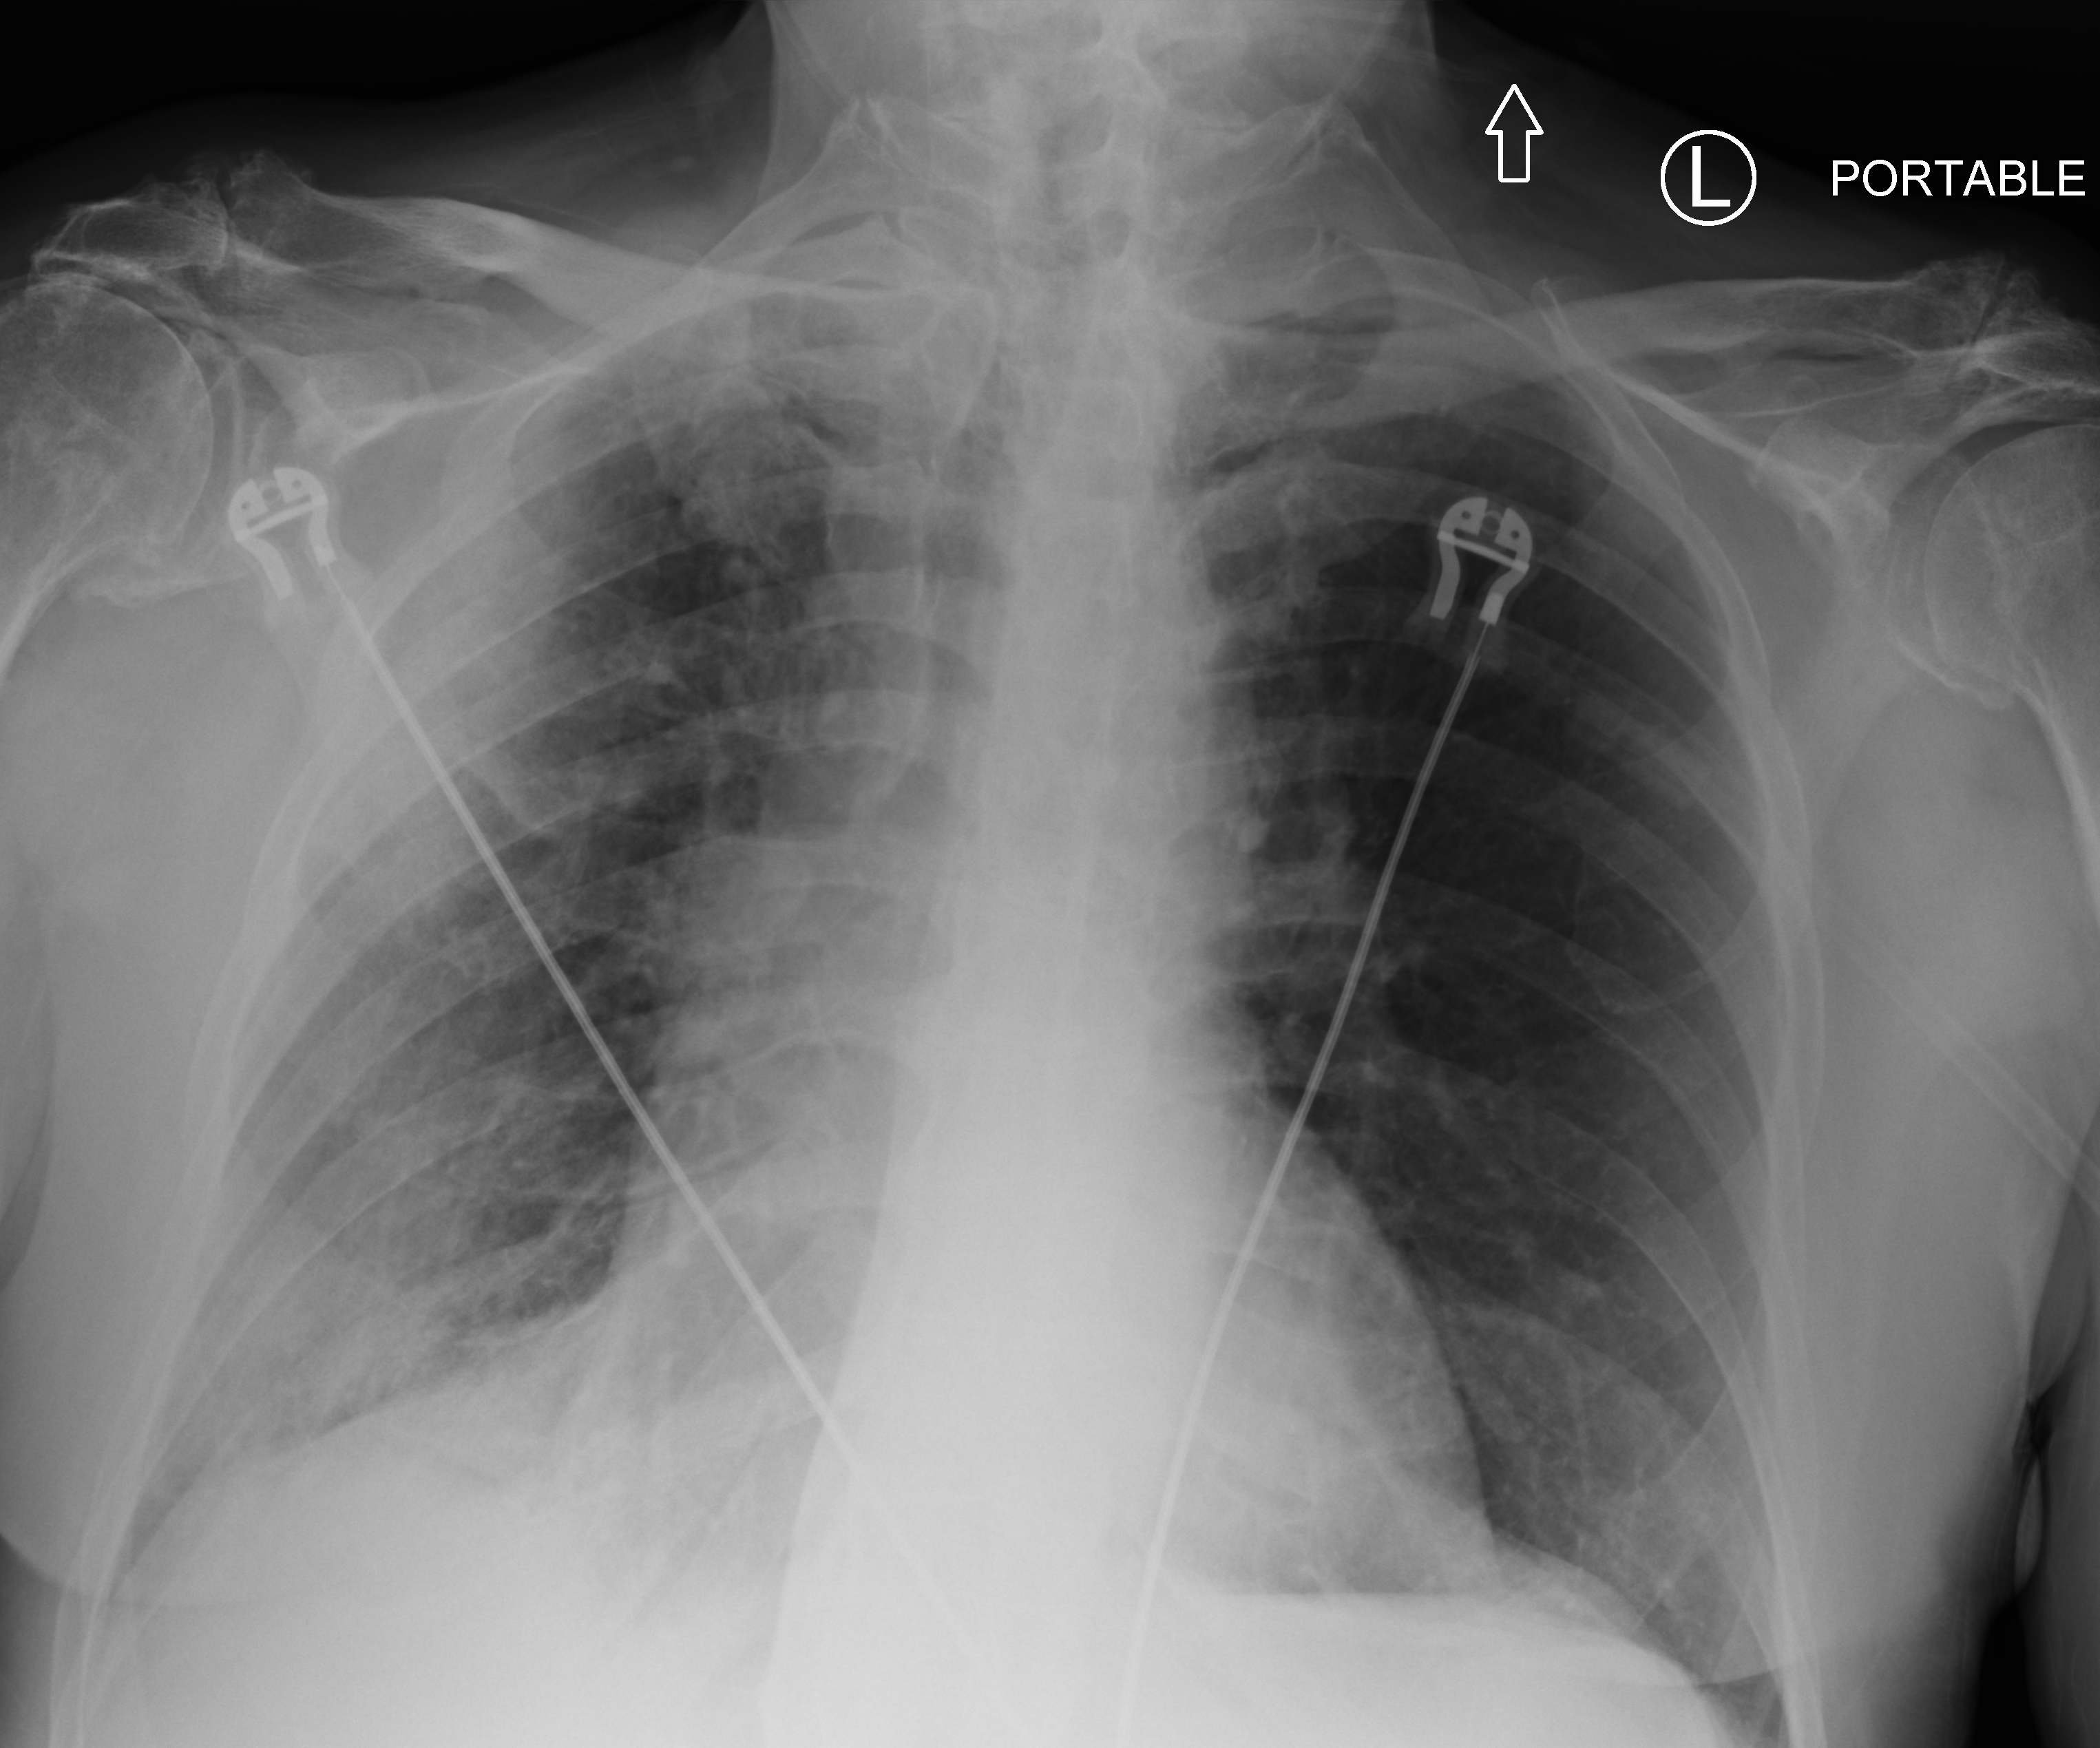
Portable chest radiograph; anteroposterior (AP) projection. Patient hospitalised with COVID-19; male, aged 75–90 years.
Admission-level facts for this patient (not findings on this image; timing relative to this image not recorded): smoking status (admission record): former.